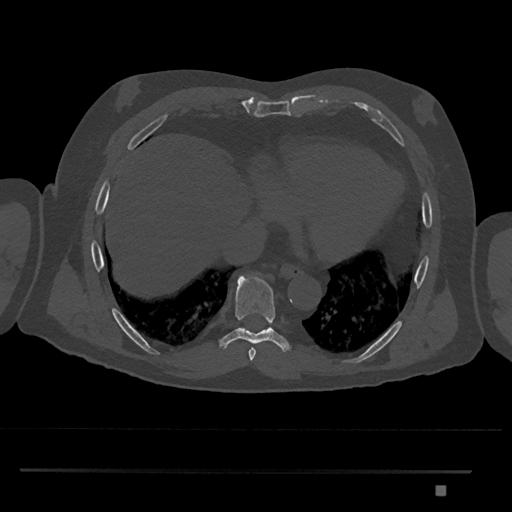
CT including the spine, one axial slice; slice 1112 of 1134 in the series (ordered by position); reconstruction kernel Br40s/3; bone window (W 1800 / L 400 HU); 0.5 mm slice thickness; 512 × 512 image matrix. Patient: male, 65 years. From the clinical record (not read from this slice): primary cancer: prostate.
Outlined on this slice (semi-automatic segmentation, software-assisted and operator-edited):
- T8 vertebra: bounding box [x1, y1, x2, y2] px = [219, 275, 291, 352]